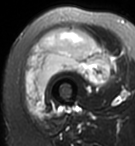
MRI of an extremity soft-tissue mass, one axial slice. Position 34 of 95 along the scan axis. T2-weighted fat-saturated. MR volume resampled by the dataset authors to the PET/CT grid (not the native acquisition matrix). 135 × 146 image matrix. Female patient. Case-level facts recorded for this patient, not image findings: histological type: pleiomorphic undifferentiated sarcoma; grade: high; site of the primary tumour: right quadricep.
Structures marked on this image (expert contour drawn on MRI and transferred to this co-registered scan by the dataset authors):
- gross tumour volume including surrounding oedema: bounding box <25,29,109,115> (left, top, right, bottom; pixels)
- gross tumour volume (mass): <25,29,109,115>